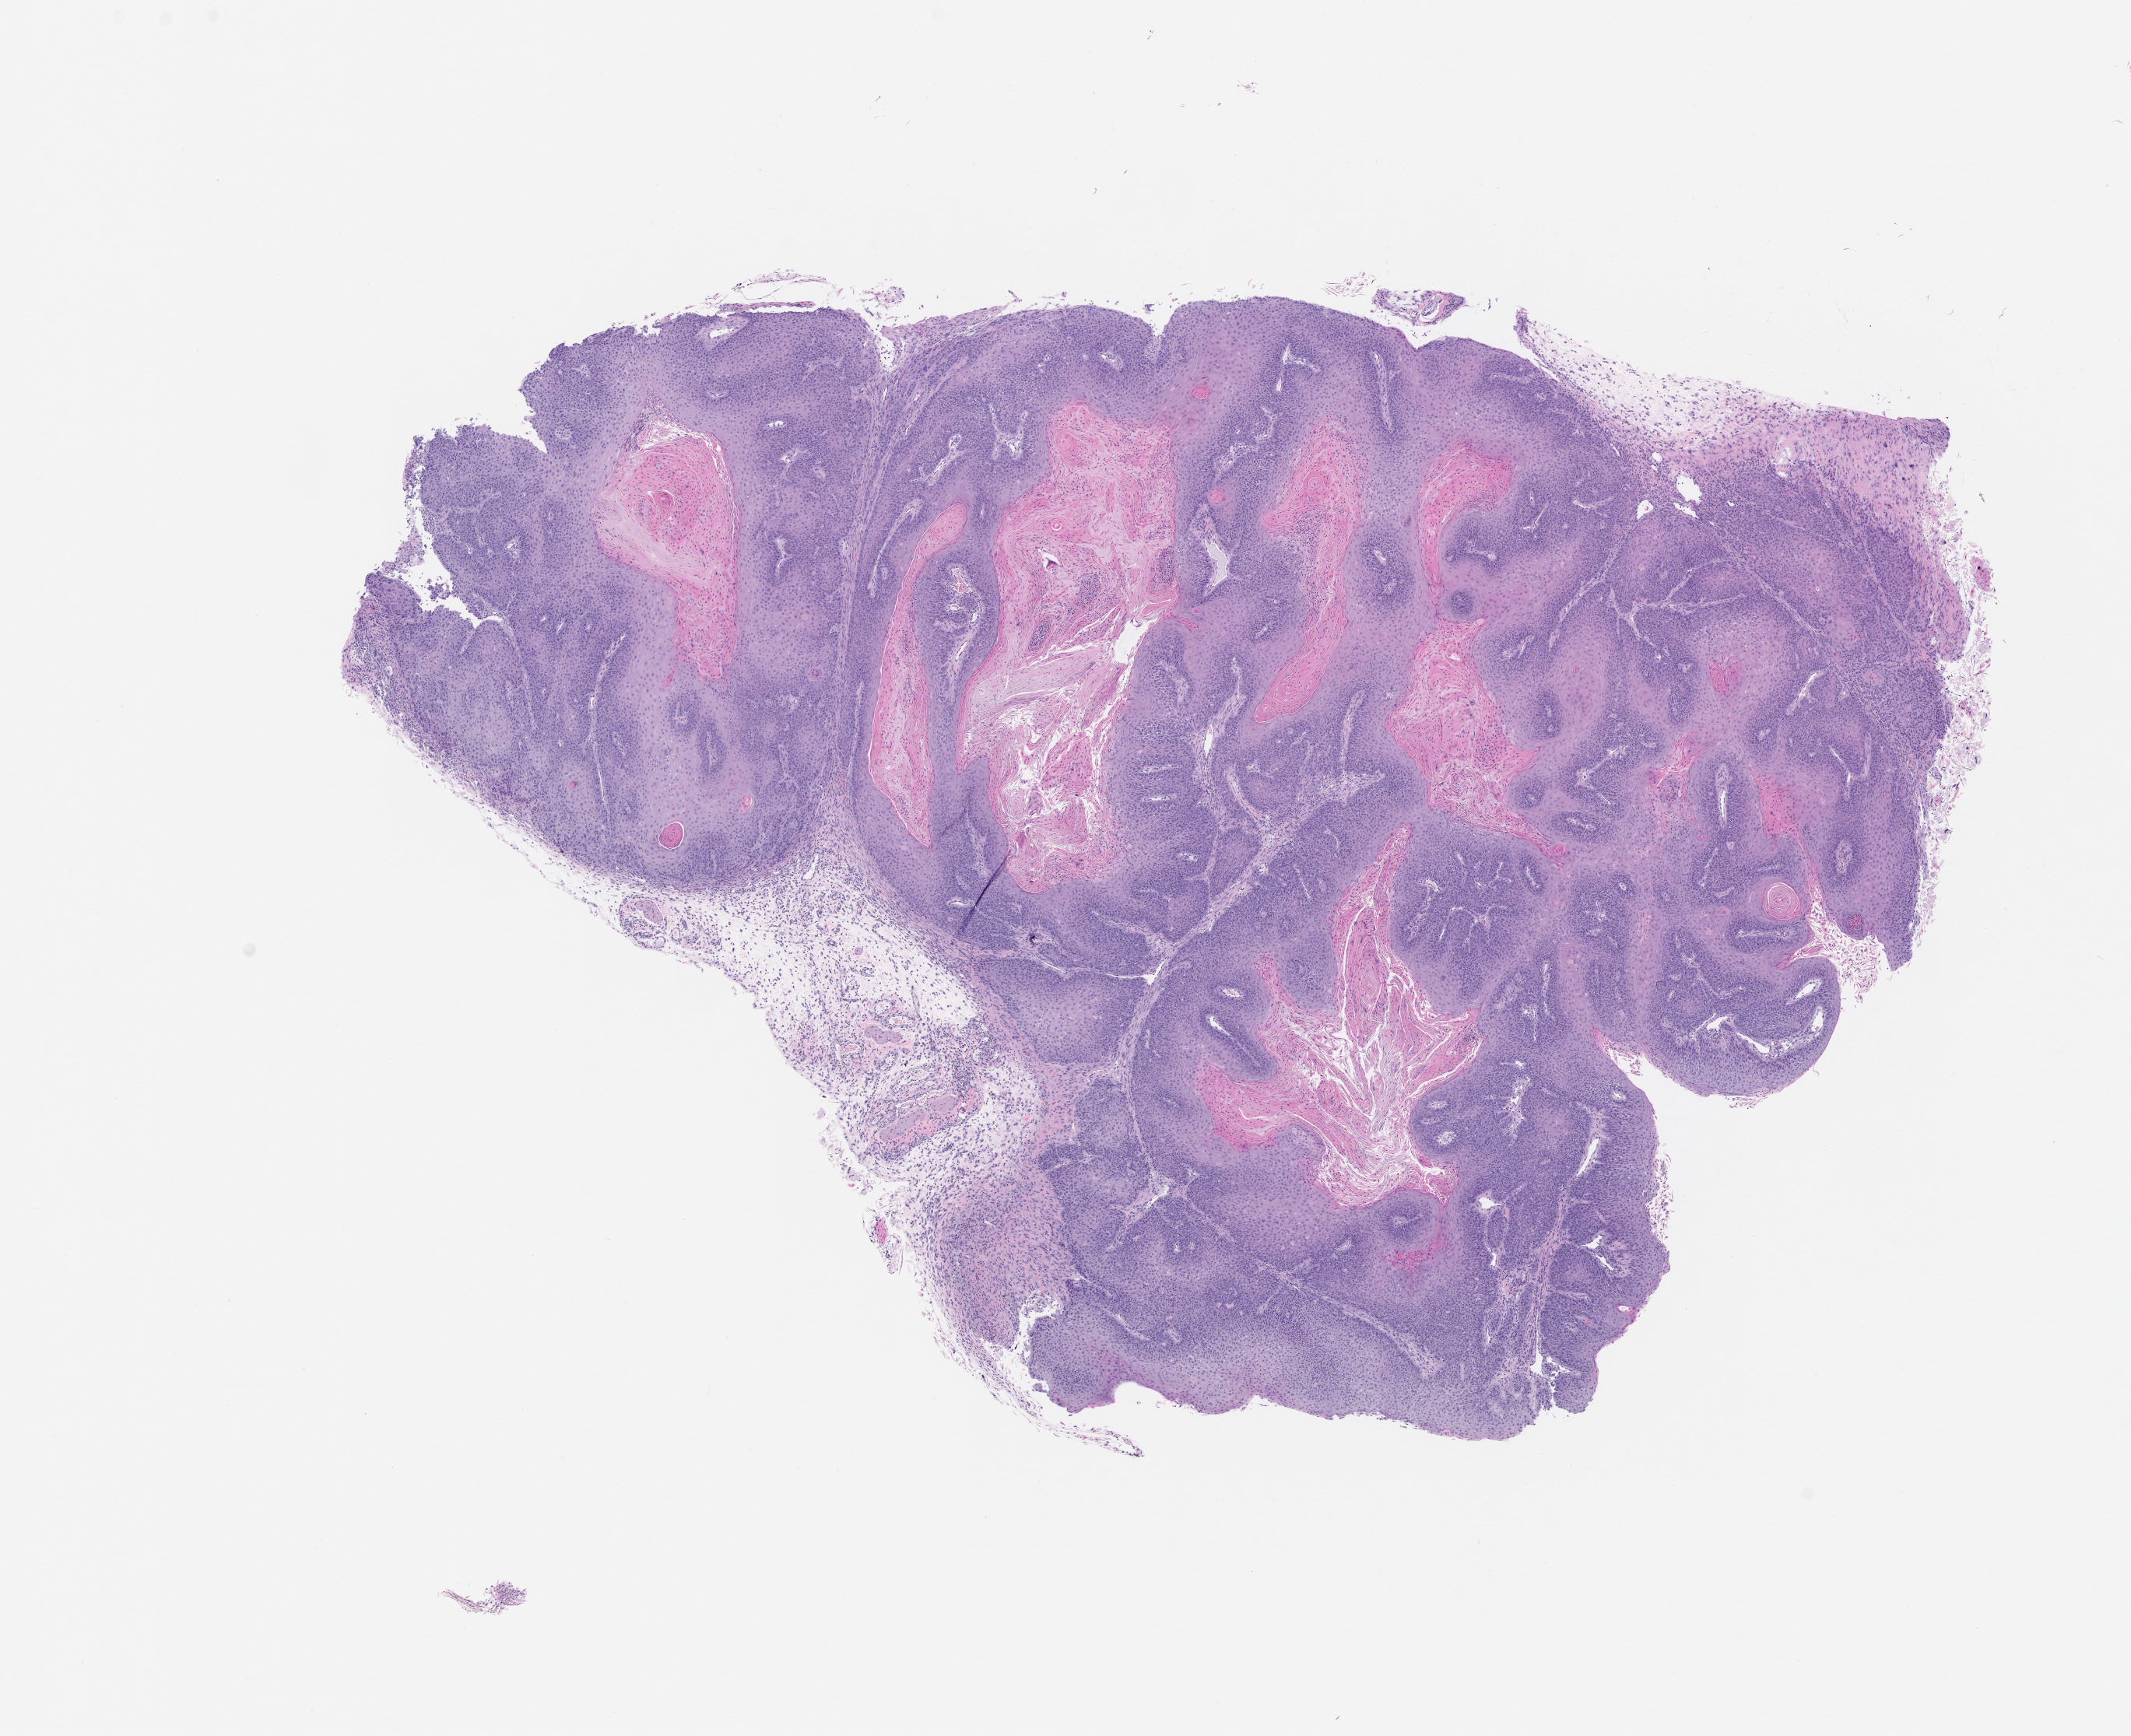
Whole-slide image, haematoxylin and eosin: patient-derived xenograft (human tumor grown in a mouse), passage 0, whole scanned area (about 11.0 x 8.9 mm) shown as a low-resolution overview, formalin-fixed, paraffin-embedded (FFPE) tissue, originating tumor site category: bladder.
Originating patient diagnosis: Transitional Cell Carcinoma.